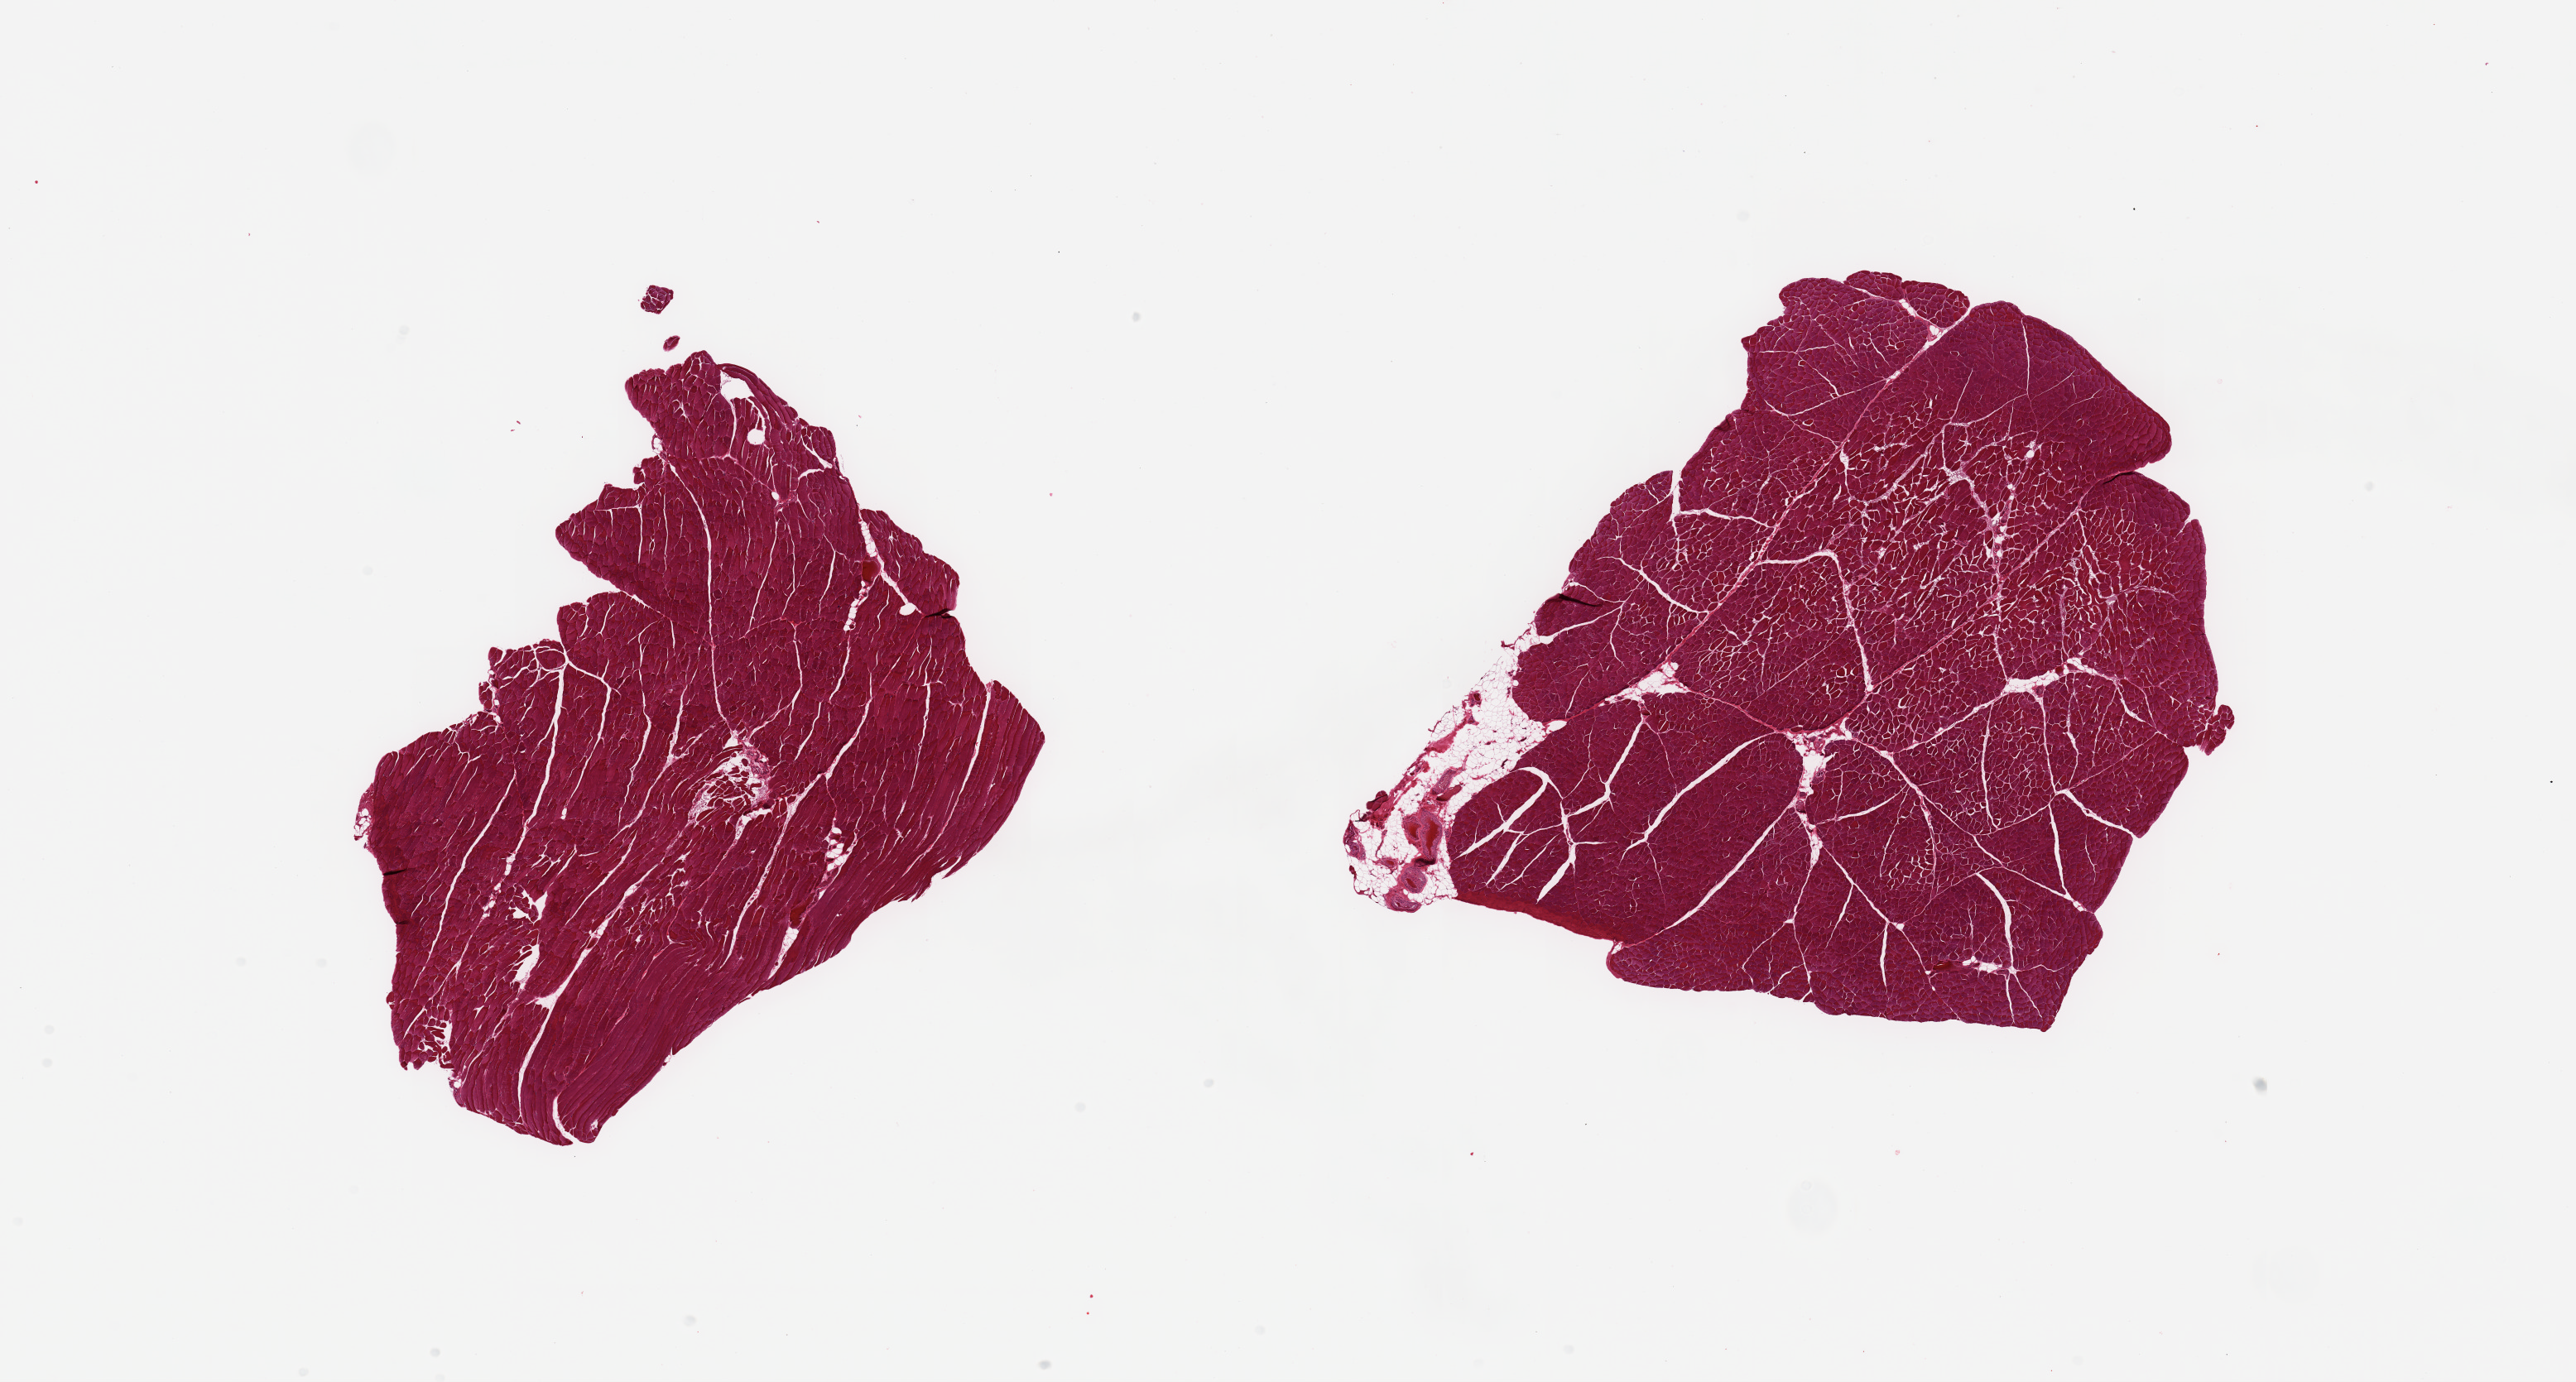
Whole-slide image, haematoxylin and eosin stain, brightfield, shown as a low-resolution overview of the whole scanned area (about 24.6 x 13.2 mm, slide scanned at 20x); PAXgene-fixed paraffin-embedded (PFPE) section; target tissue: skeletal muscle; donor tissue sample. Male donor.
Review note (as recorded): 2 pieces.